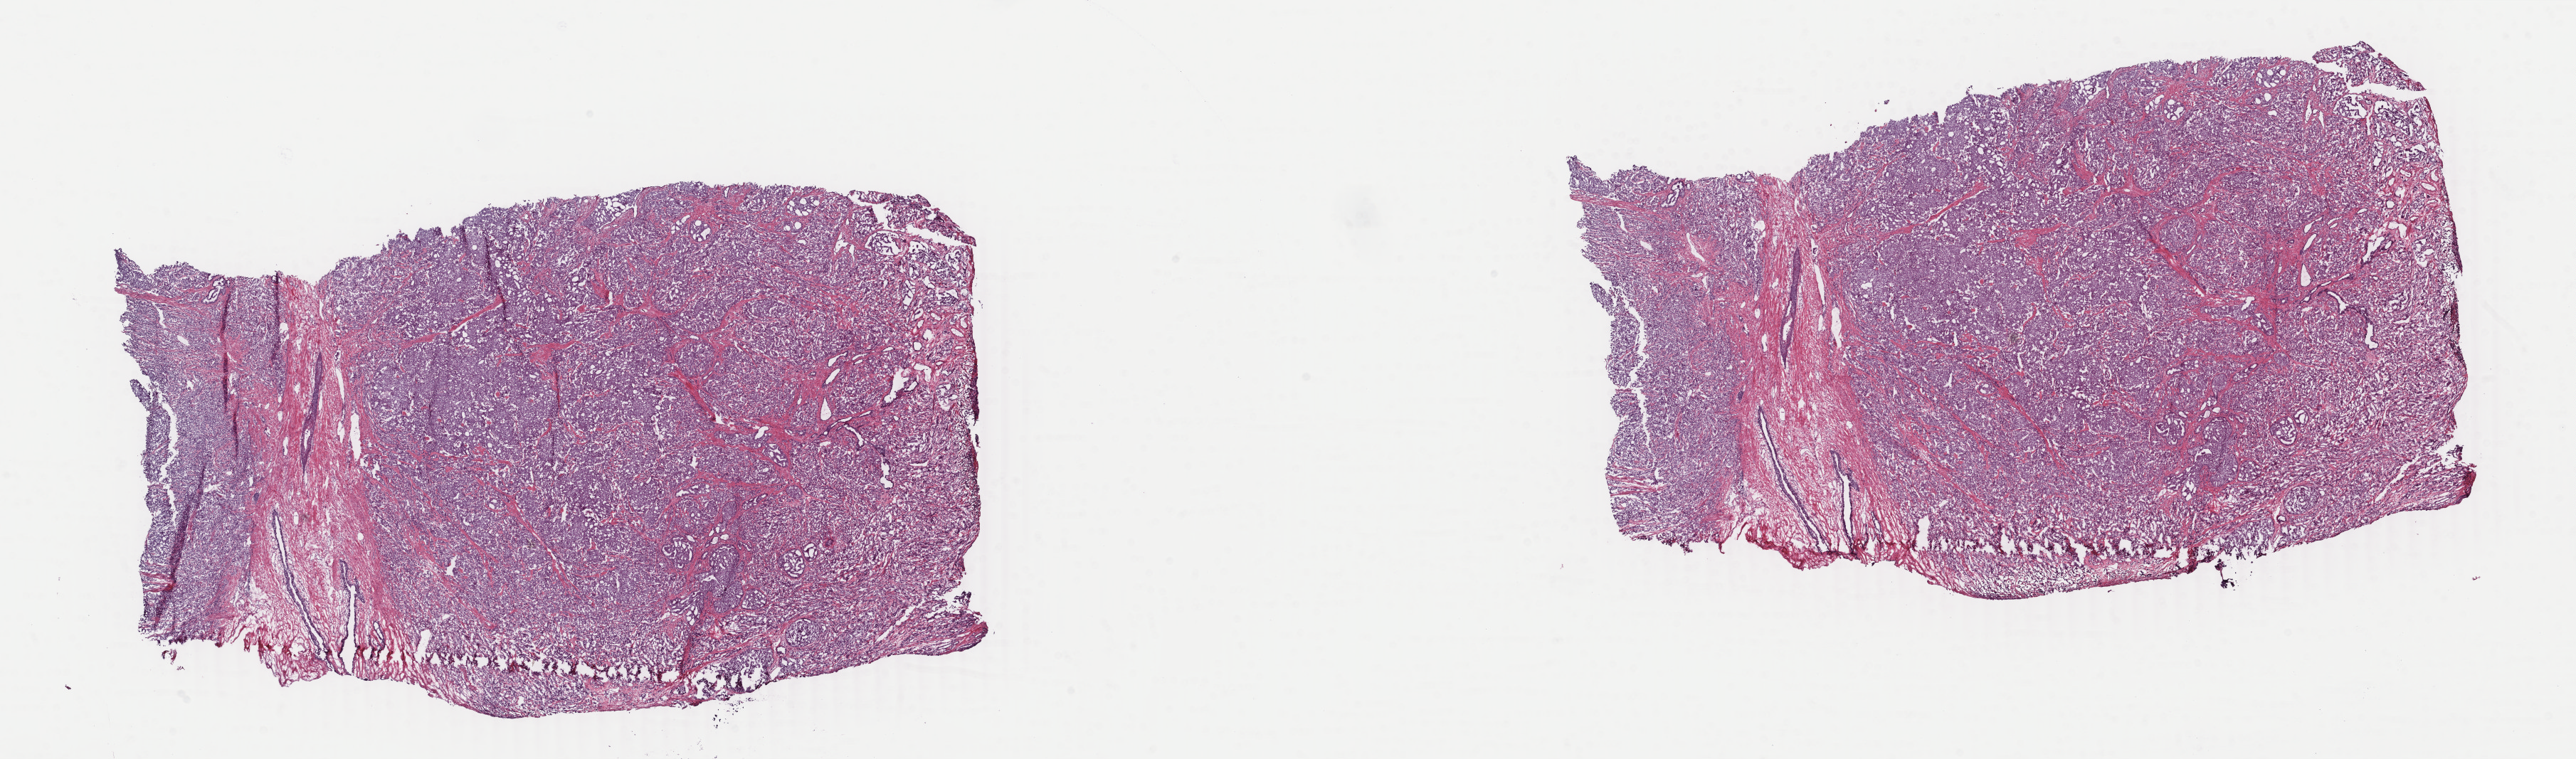
Whole-slide histology image, H&E — a low-resolution overview of the entire scanned area, about 28.8 x 8.5 mm. Frozen section from the top of the tissue portion. Sample: primary tumour, prostate. Male, age 53 years at initial diagnosis. Gleason score: 9 (4+5). Pathologist review of this section (percent, as recorded): tumour cells 85%, tumour nuclei 90%, normal cells 2%, stromal cells 13%, necrosis 0%. Infiltration values recorded for this section: lymphocyte infiltration 0%, monocyte infiltration 0%, neutrophil infiltration 0%.
Diagnosis: Adenocarcinoma, NOS (prostate gland). Lymph nodes positive (case pathology): 0 of 9 examined.